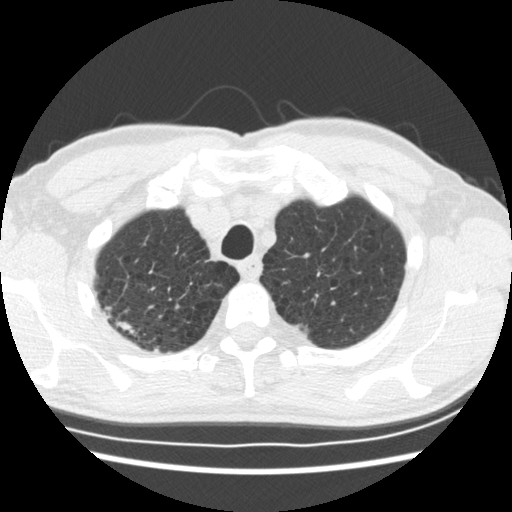
Low-dose screening chest CT, one axial slice. Position 154 of 183 along the scan axis. Reconstruction kernel STANDARD. Lung window (W 1500 / L -600 HU). 512 × 512 image matrix, field of view 339 × 339 mm.
Structures marked on this image (manually delineated by an expert):
- lesion 1 (tumor, upper lobe of right lung): bounding box [x1, y1, x2, y2] px = [116, 318, 140, 337]